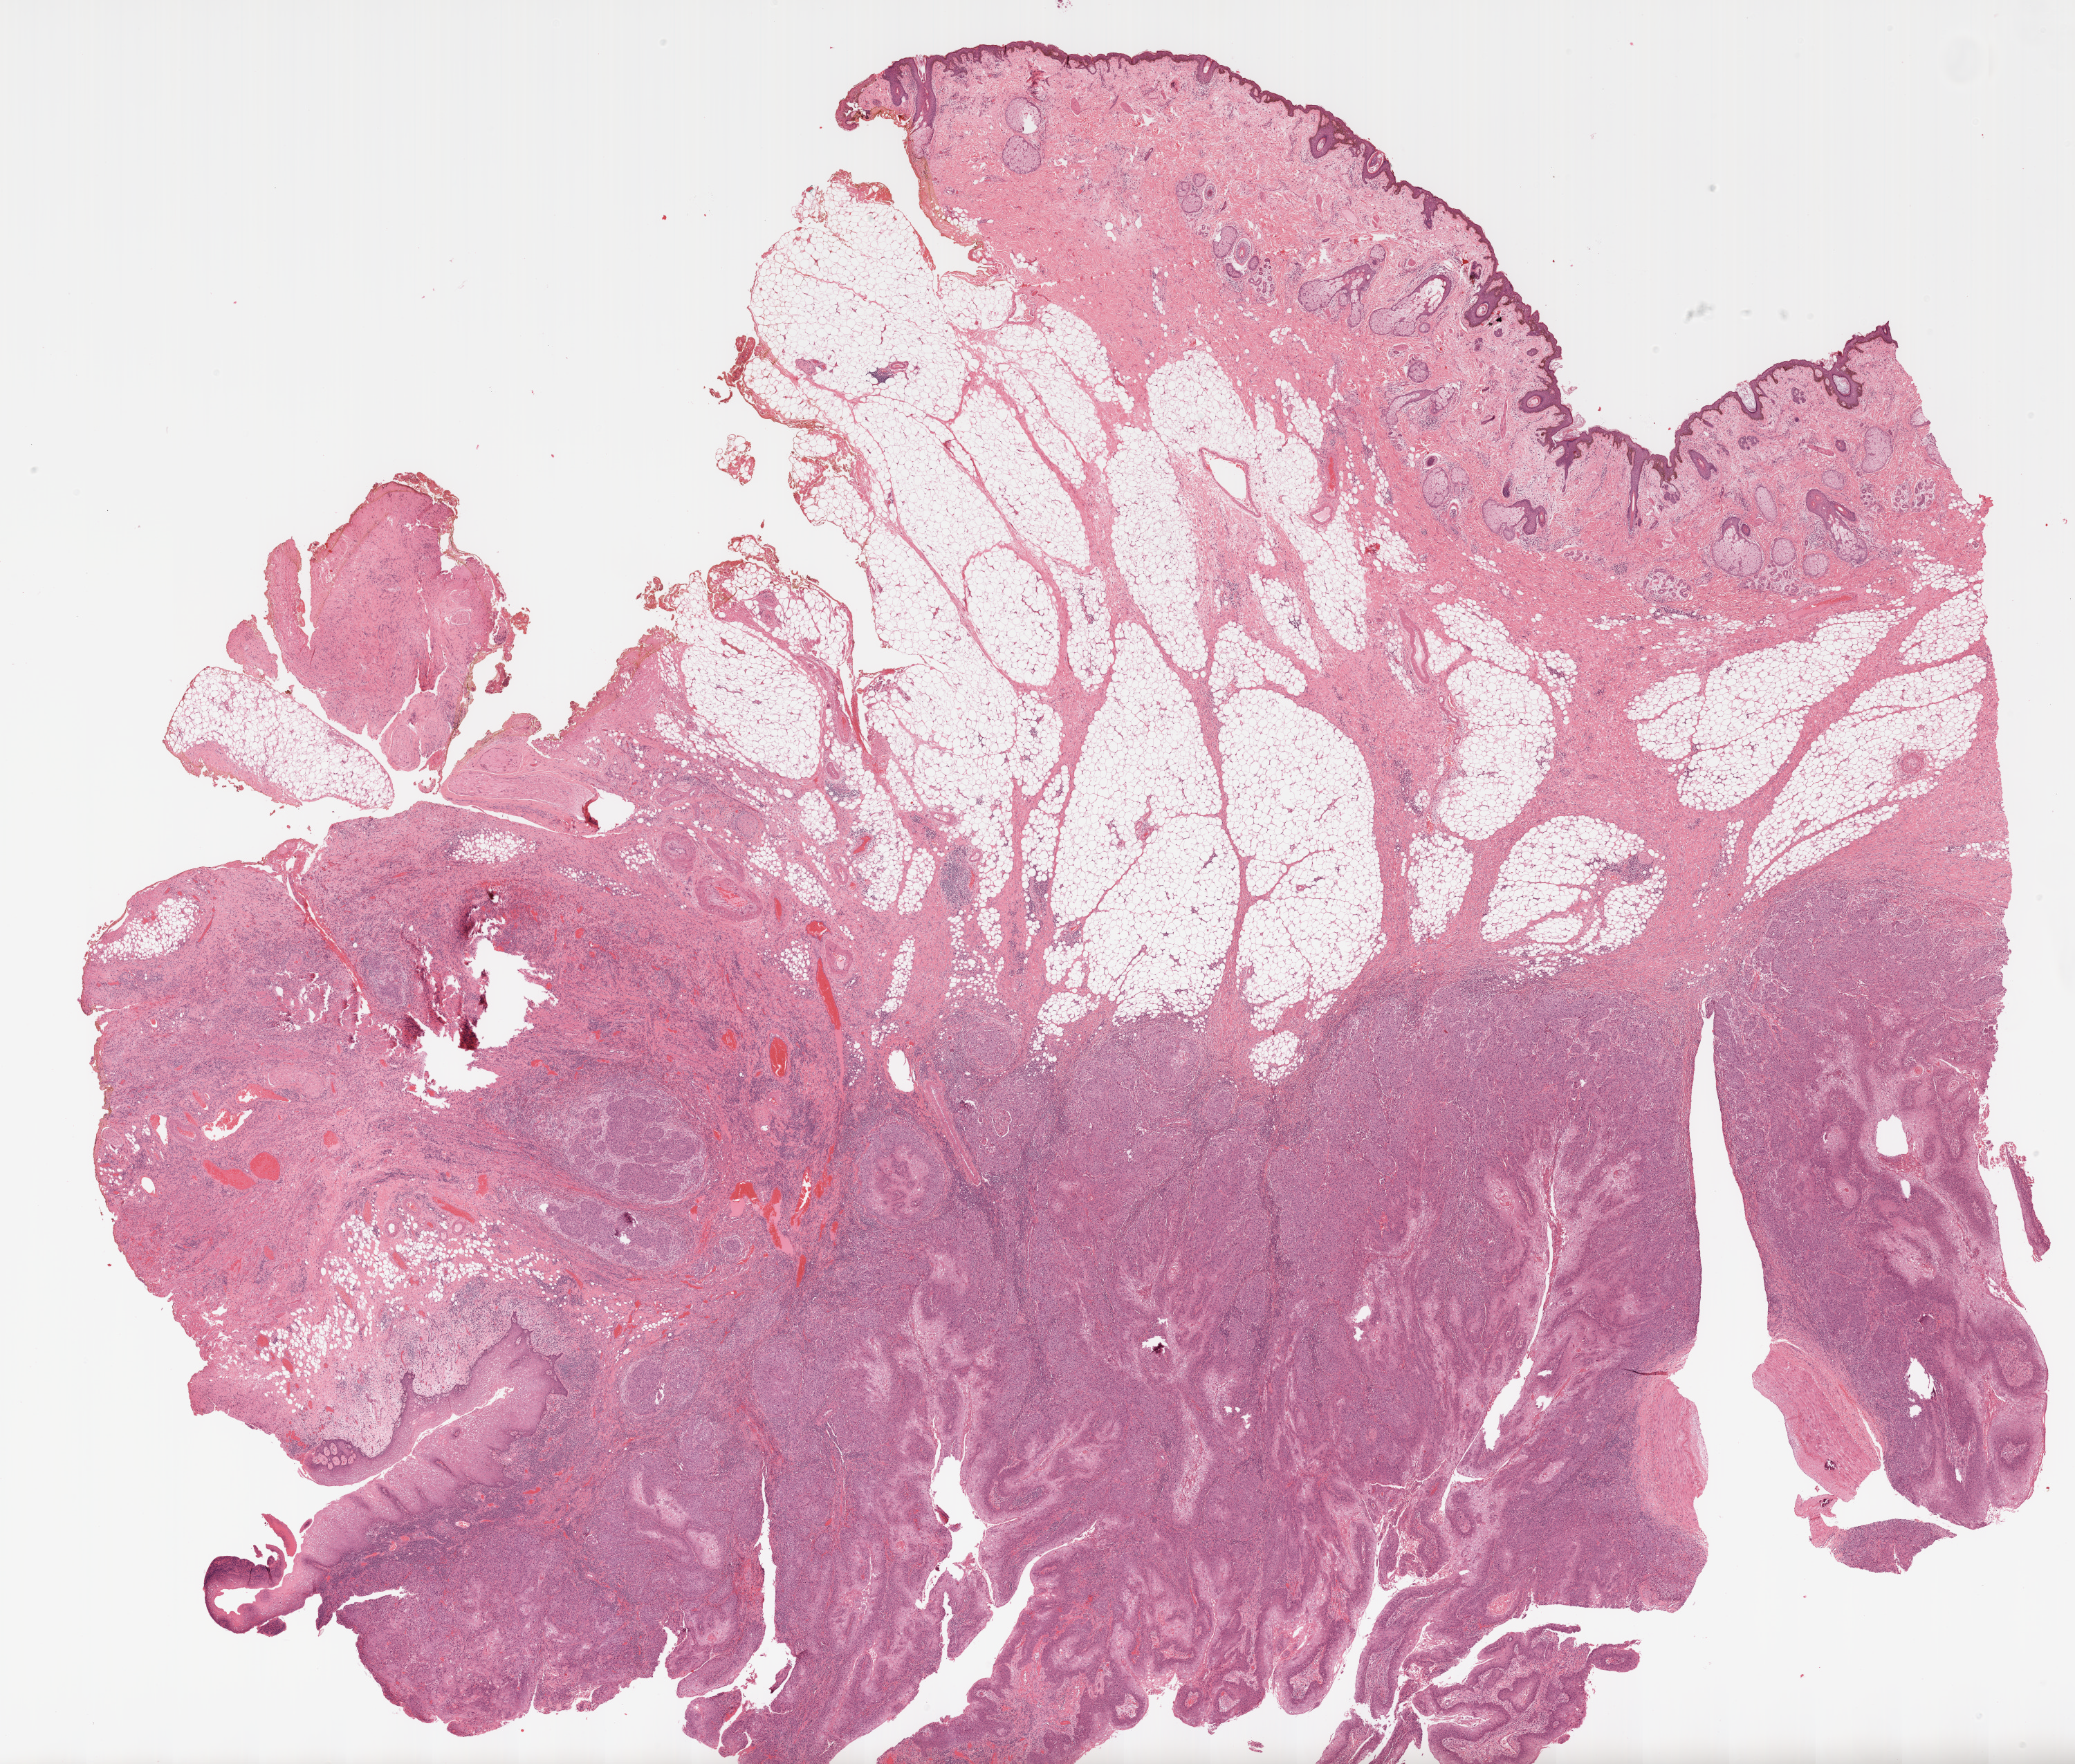
Digitized Hematoxylin and eosin (H&E) stained tissue section (whole slide), a low-resolution overview of the entire scanned area, about 24.1 x 20.5 mm (slide scanned at 20x), formalin-fixed paraffin-embedded (FFPE) diagnostic section, sample: primary tumour, head and neck. Patient: male, age at initial diagnosis 87 years. Histologic grade: G2 (moderately differentiated).
AJCC pathologic stage: IVA. Lymph nodes positive (case pathology): 6 of 46 examined. Pathologic diagnosis: Squamous cell carcinoma, NOS (cheek mucosa). Laterality: right.